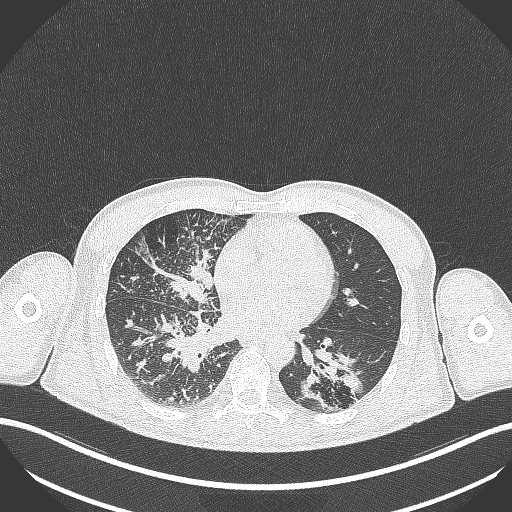
Chest CT, one axial slice; slice 136 of 348 in the series (ordered by position); reconstruction kernel B70f; 120 kVp; lung window (W 1500 / L -600 HU); 1 mm slice thickness; 512 × 512 image matrix, field of view 400 × 400 mm. Patient: male, 49 years. From the clinical record (not read from this slice): clinical TNM (as recorded): T2b N1 M0.
Outlined on this slice (bounding box drawn by a radiologist):
- lung tumour (recorded histology: adenocarcinoma): bounding box <294,342,368,411> (left, top, right, bottom; pixels)